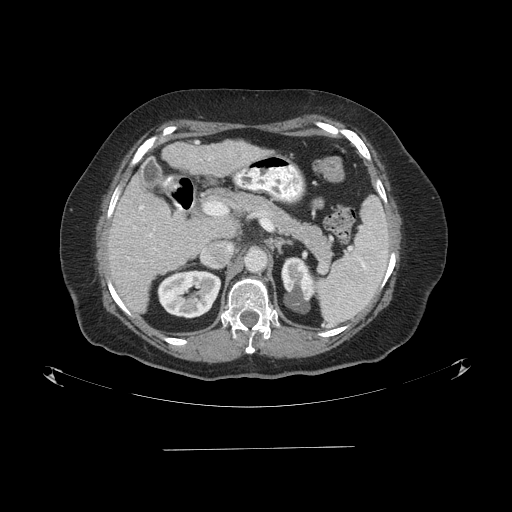
Contrast-enhanced abdominal CT (liver protocol), one axial slice; slice 46 of 103 in the series (ordered by position); one of 2 acquisitions stored at this slice position; soft-tissue window (W 400 / L 40 HU); 2.5 mm slice thickness; 512 × 512 image matrix. From the clinical record (not read from this slice): diagnosis: hepatocellular carcinoma (patient treated with transarterial chemoembolisation; whether this scan precedes or follows treatment is not stated here); TNM stage (as recorded): Stage-IIIA; Child-Pugh class: A; tumour differentiation: poorly differentiated; tumour nodularity: multinodular.
Structures marked on this image (semi-automatically segmented with operator editing):
- liver parenchyma outside the tumour (the mass and vessels are separate outlines, so this box may not span the whole liver): bounding box [x1, y1, x2, y2] px = [106, 140, 260, 312]
- liver vessels: [140, 206, 152, 237]